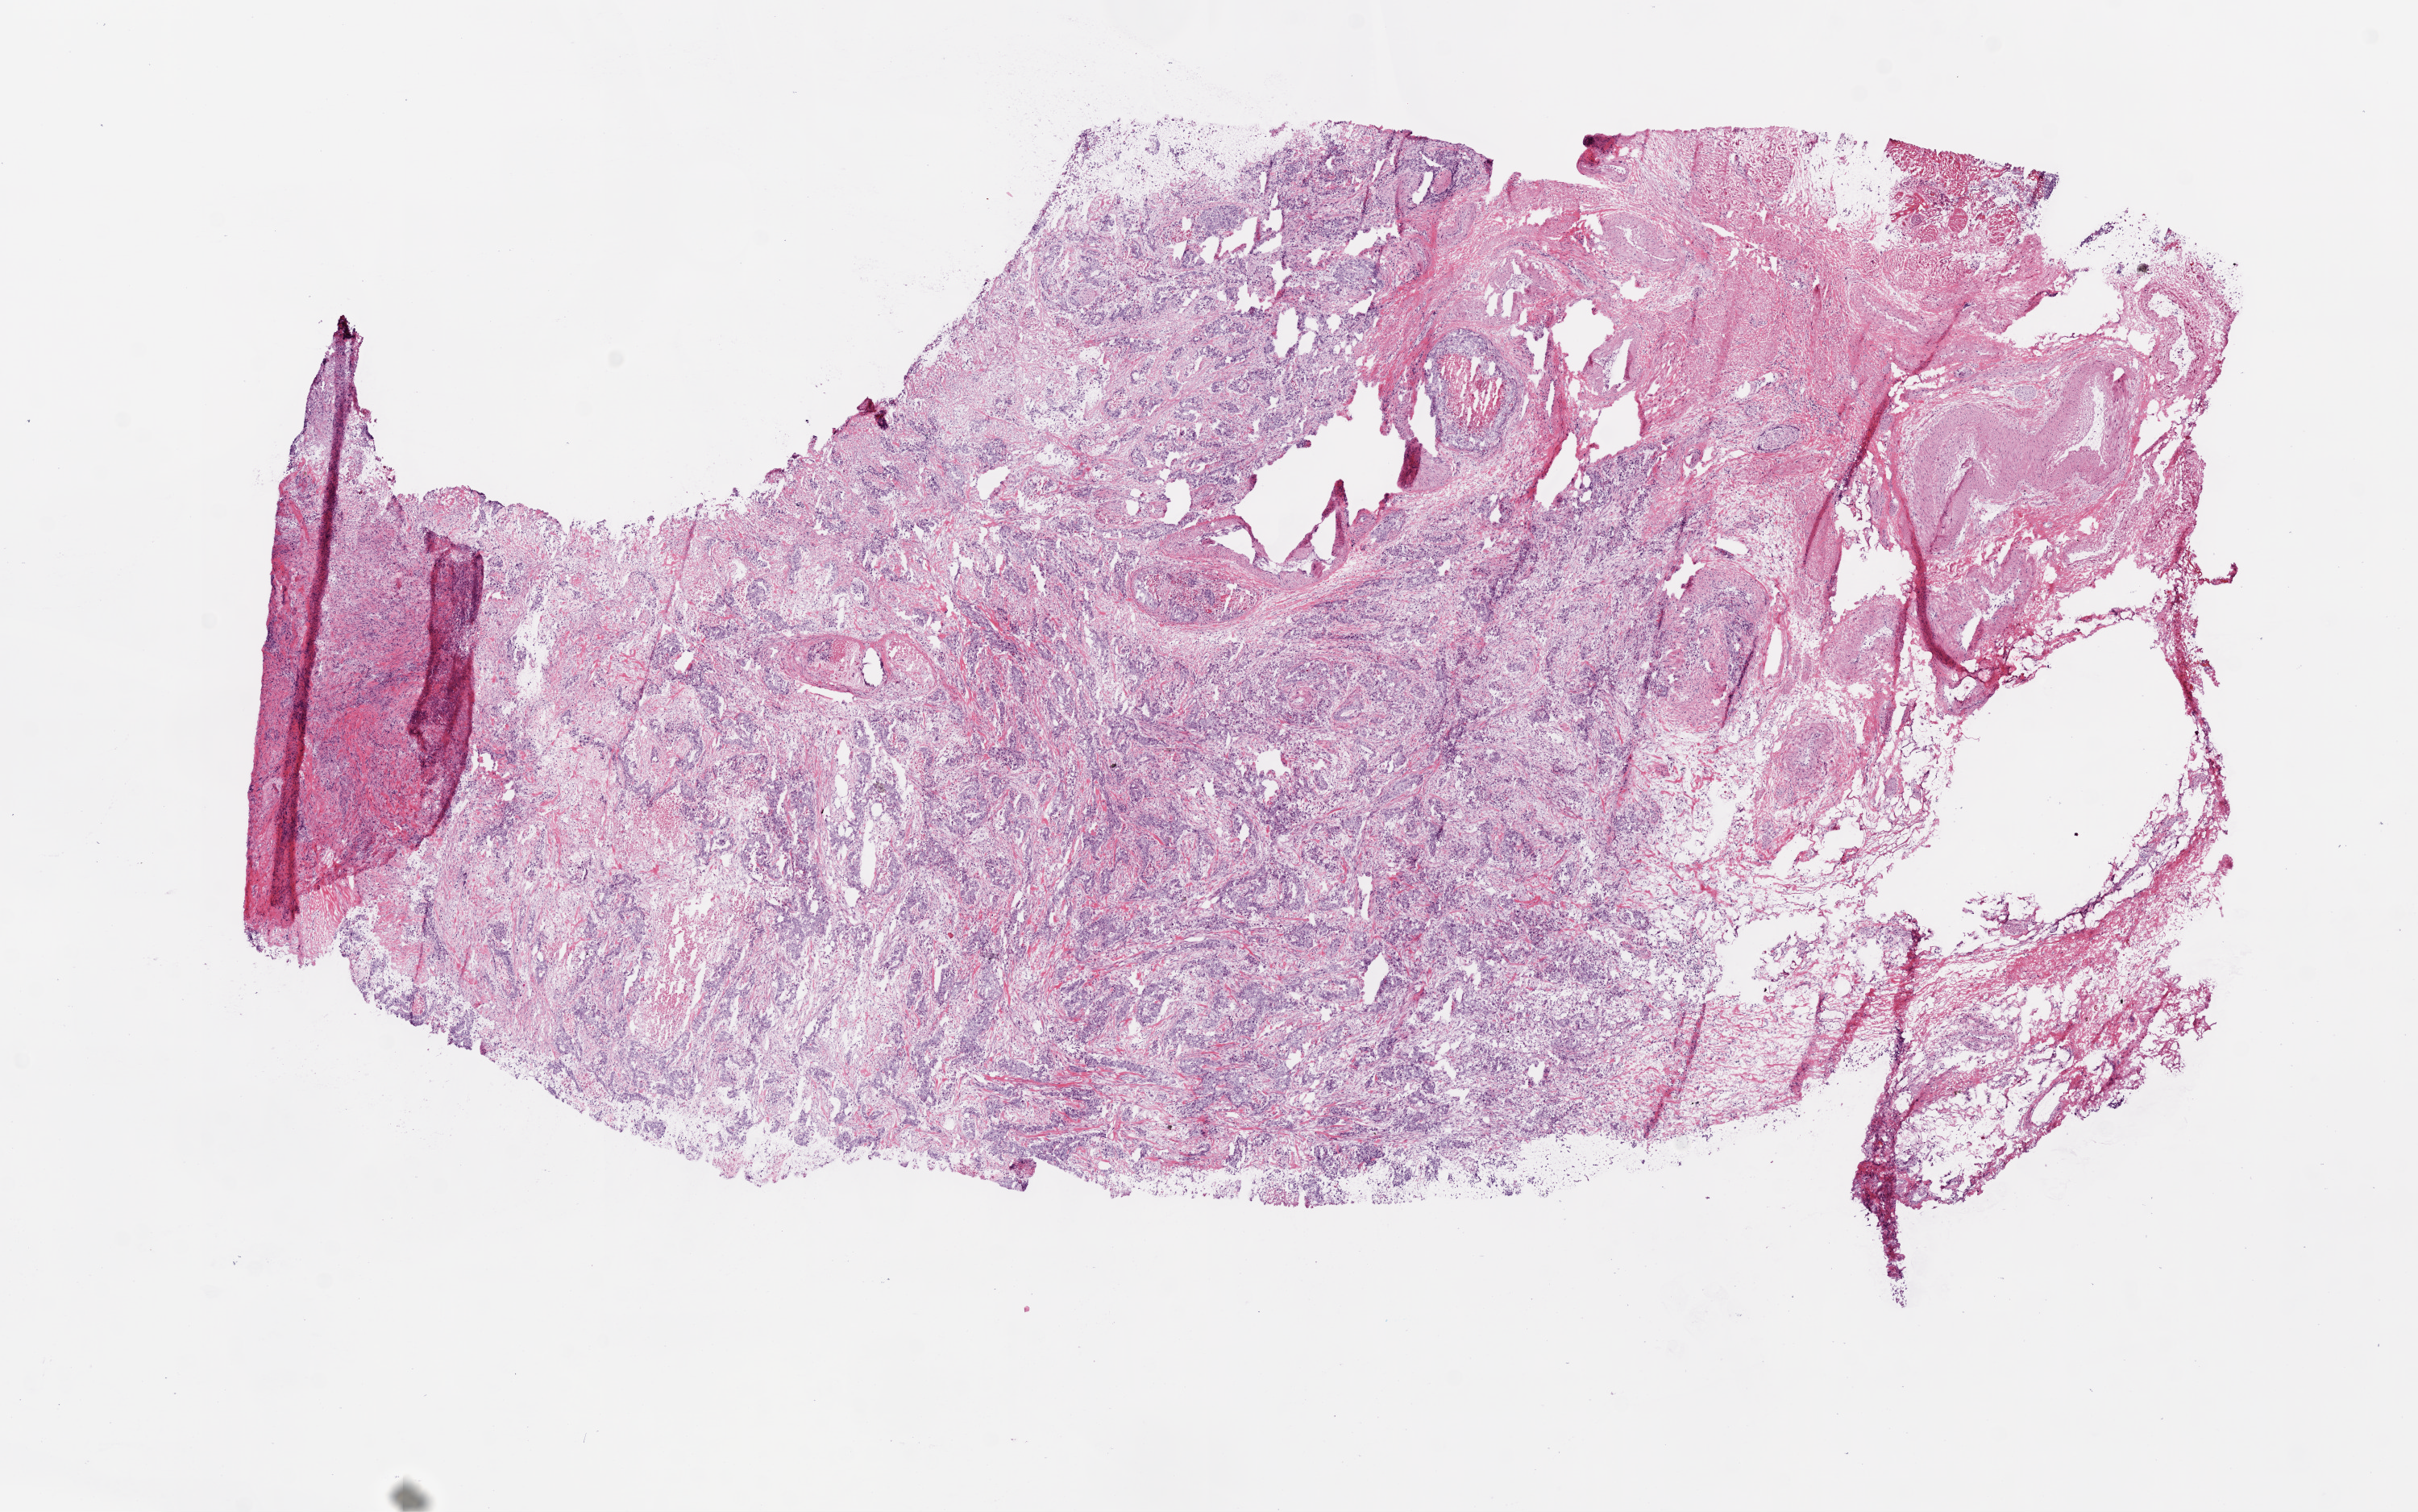
Digitized Hematoxylin and eosin (H&E) stained tissue section (whole slide) — low-resolution overview of the scanned area, about 12.0 x 7.5 mm (acquisition: 20x scan); frozen section from the top of the tissue portion; rectum, primary tumour sample. Male patient; age at initial diagnosis 39 years. Slide review estimates, as recorded: tumour cells 65%, tumour nuclei 75%, normal cells 20%, stromal cells 10%, necrosis 5%.
Pathologic diagnosis: Adenocarcinoma, NOS (rectosigmoid junction). Lymph nodes positive (case pathology): 5 of 55 examined. AJCC pathologic stage: IIIB. TNM: T3 N2a M0.